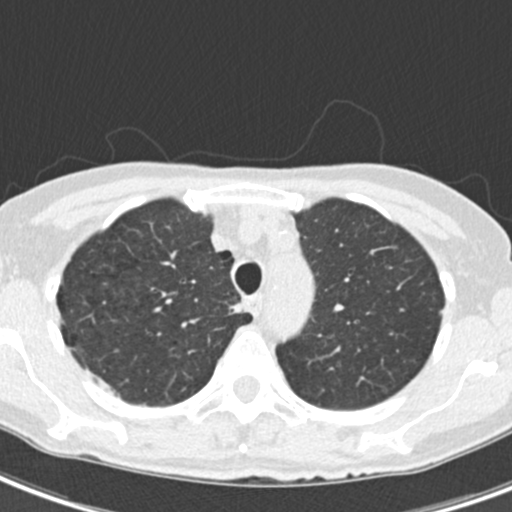
Chest CT (low-dose screening protocol), one axial image. Second annual screen. Lung window (W 1500 / L -600 HU). Standard (soft-tissue) reconstruction kernel (B30f). Slice 45 of 218 in the series. 512 × 512 image matrix. Female, age 68 years at enrolment. Current smoker at enrolment.
Expert-annotated lung lesion, bounding box <227,300,253,324> (left, top, right, bottom; pixels). No non-calcified nodule or mass ≥4 mm was recorded by the screening reader at this exam. Official screen result: negative screen, no significant abnormalities. Later outcome: lung cancer diagnosed 436 days after this screen — squamous cell carcinoma, NOS, right upper lobe, mediastinum, poorly differentiated (G3), stage IIIB (AJCC 6th edition), 43 mm at pathology.